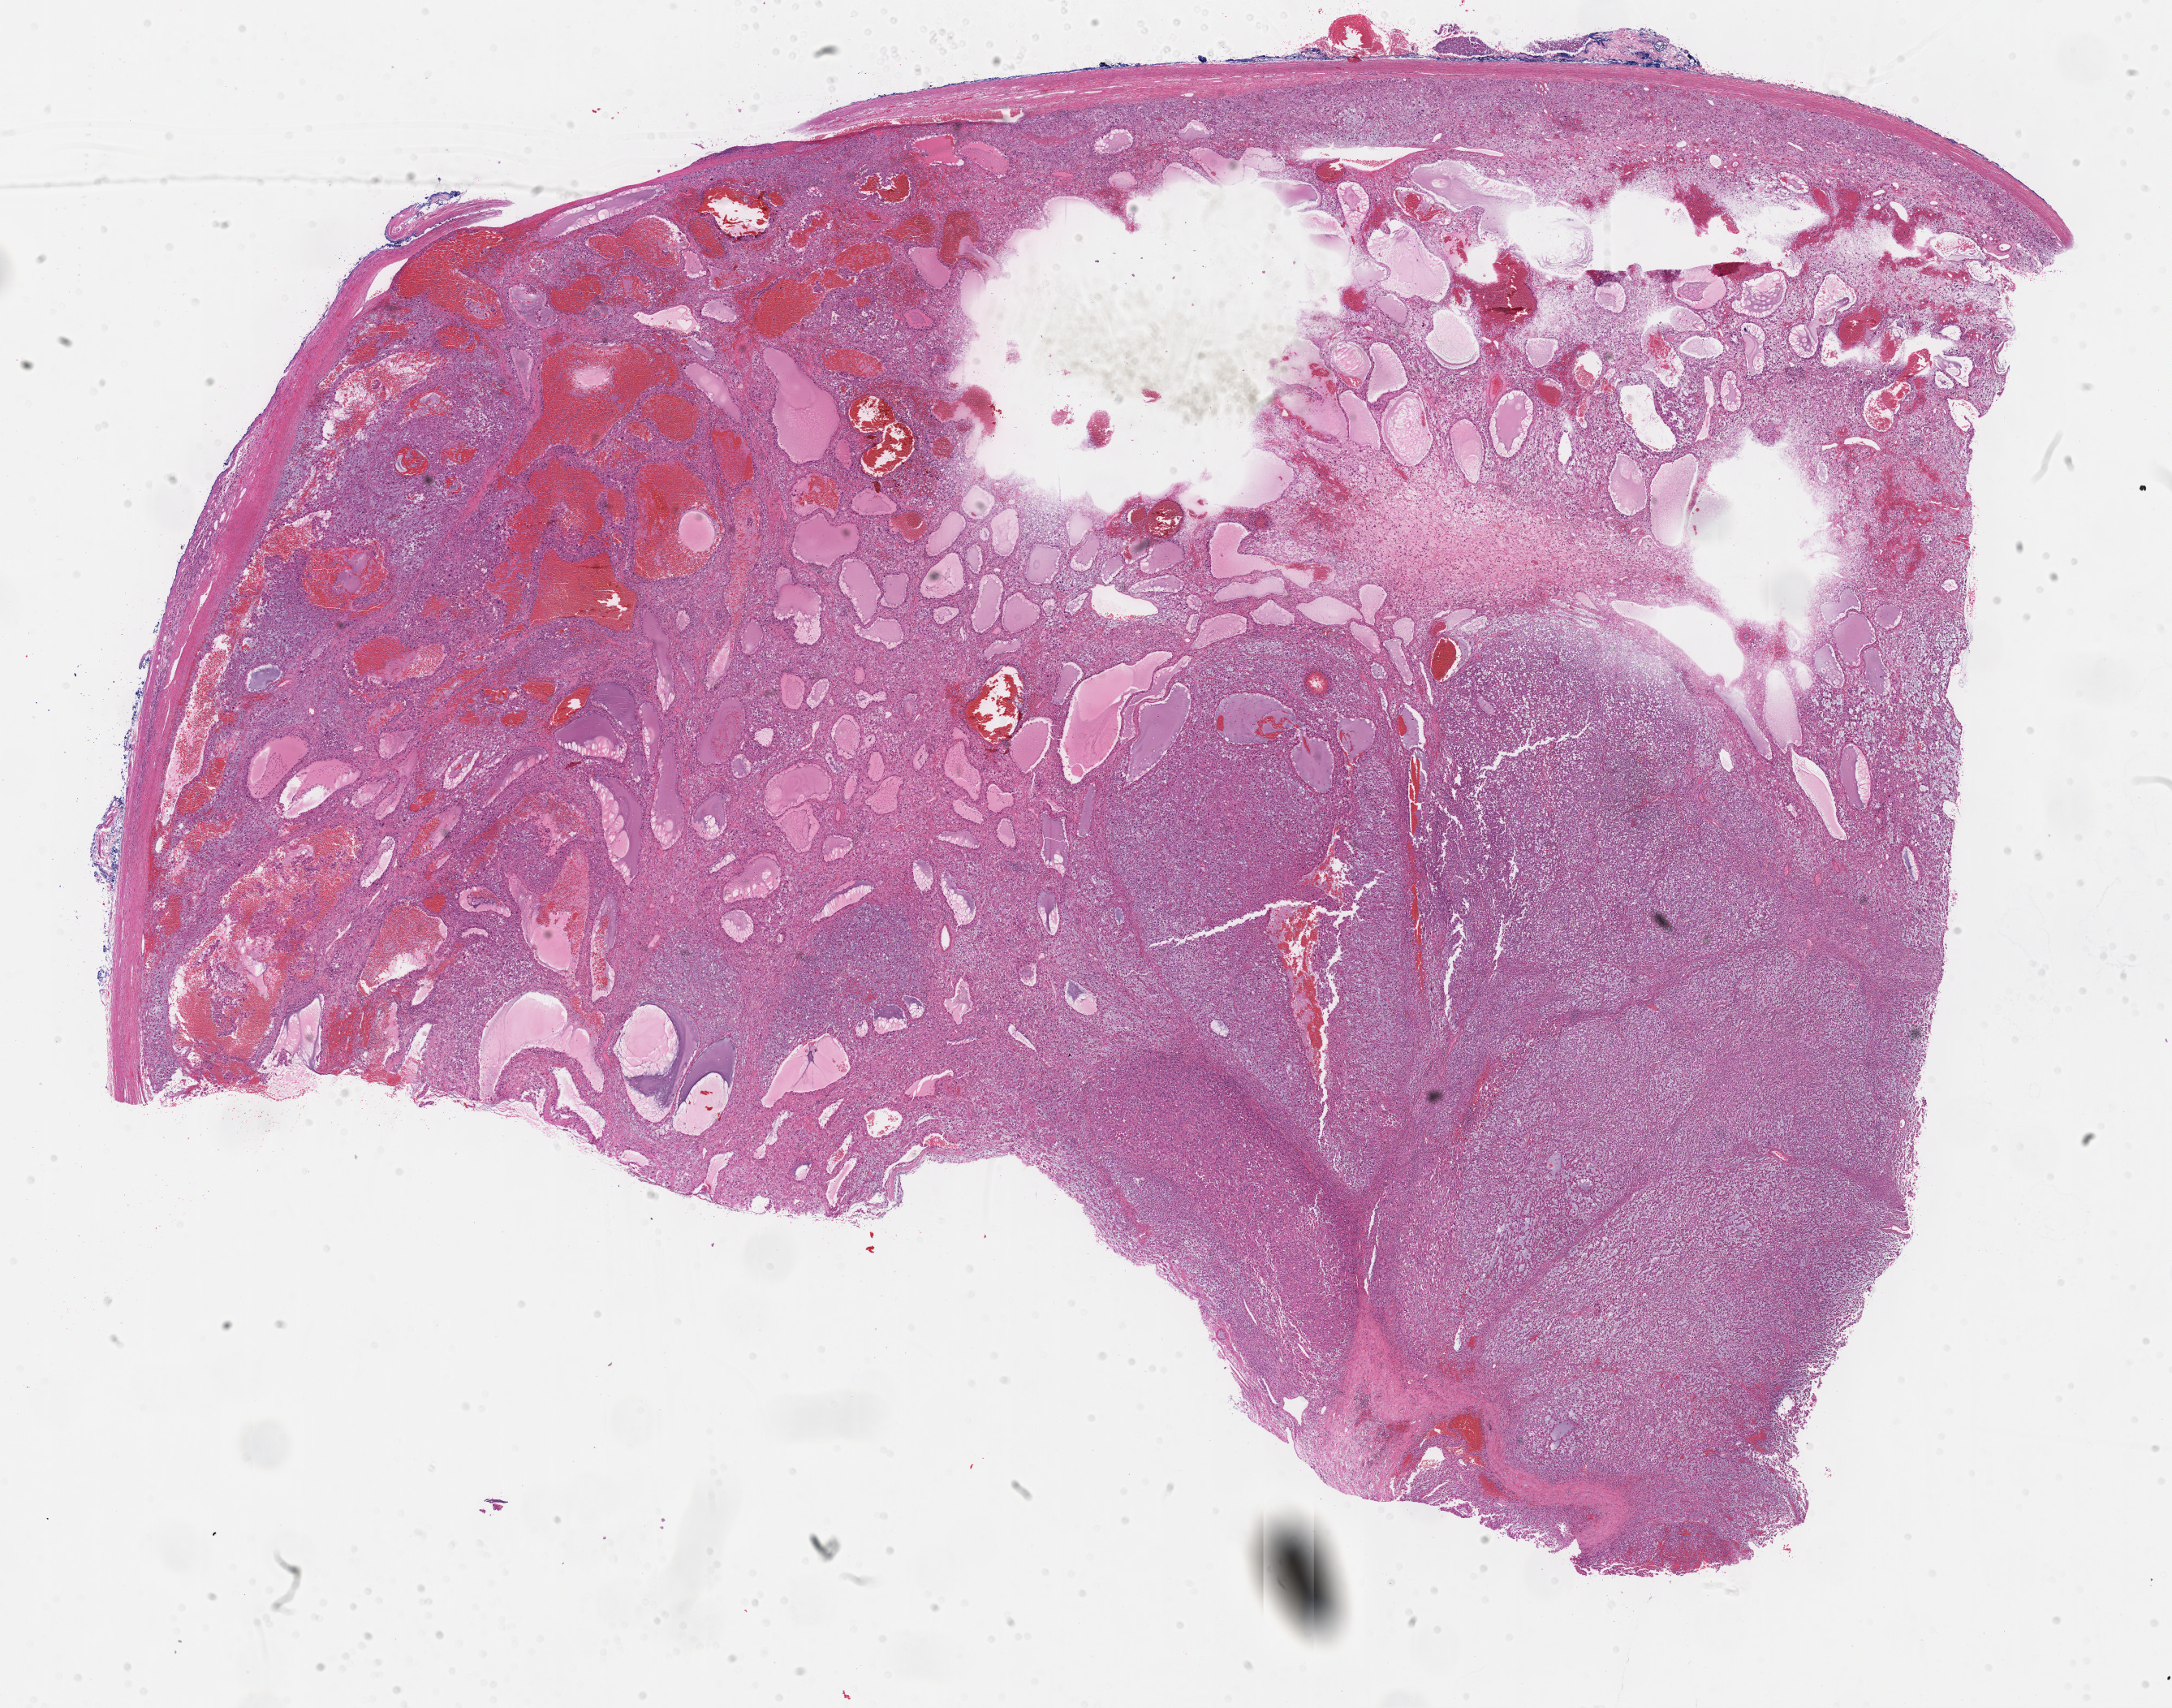
Whole-slide histology image, H&E-stained, a low-resolution overview of the entire scanned area, about 21.6 x 17.0 mm, formalin-fixed paraffin-embedded (FFPE) diagnostic section, adrenal cortex, primary tumour sample. Female patient; age at initial diagnosis 26 years.
- laterality: right
- diagnosis: Adrenal cortical carcinoma